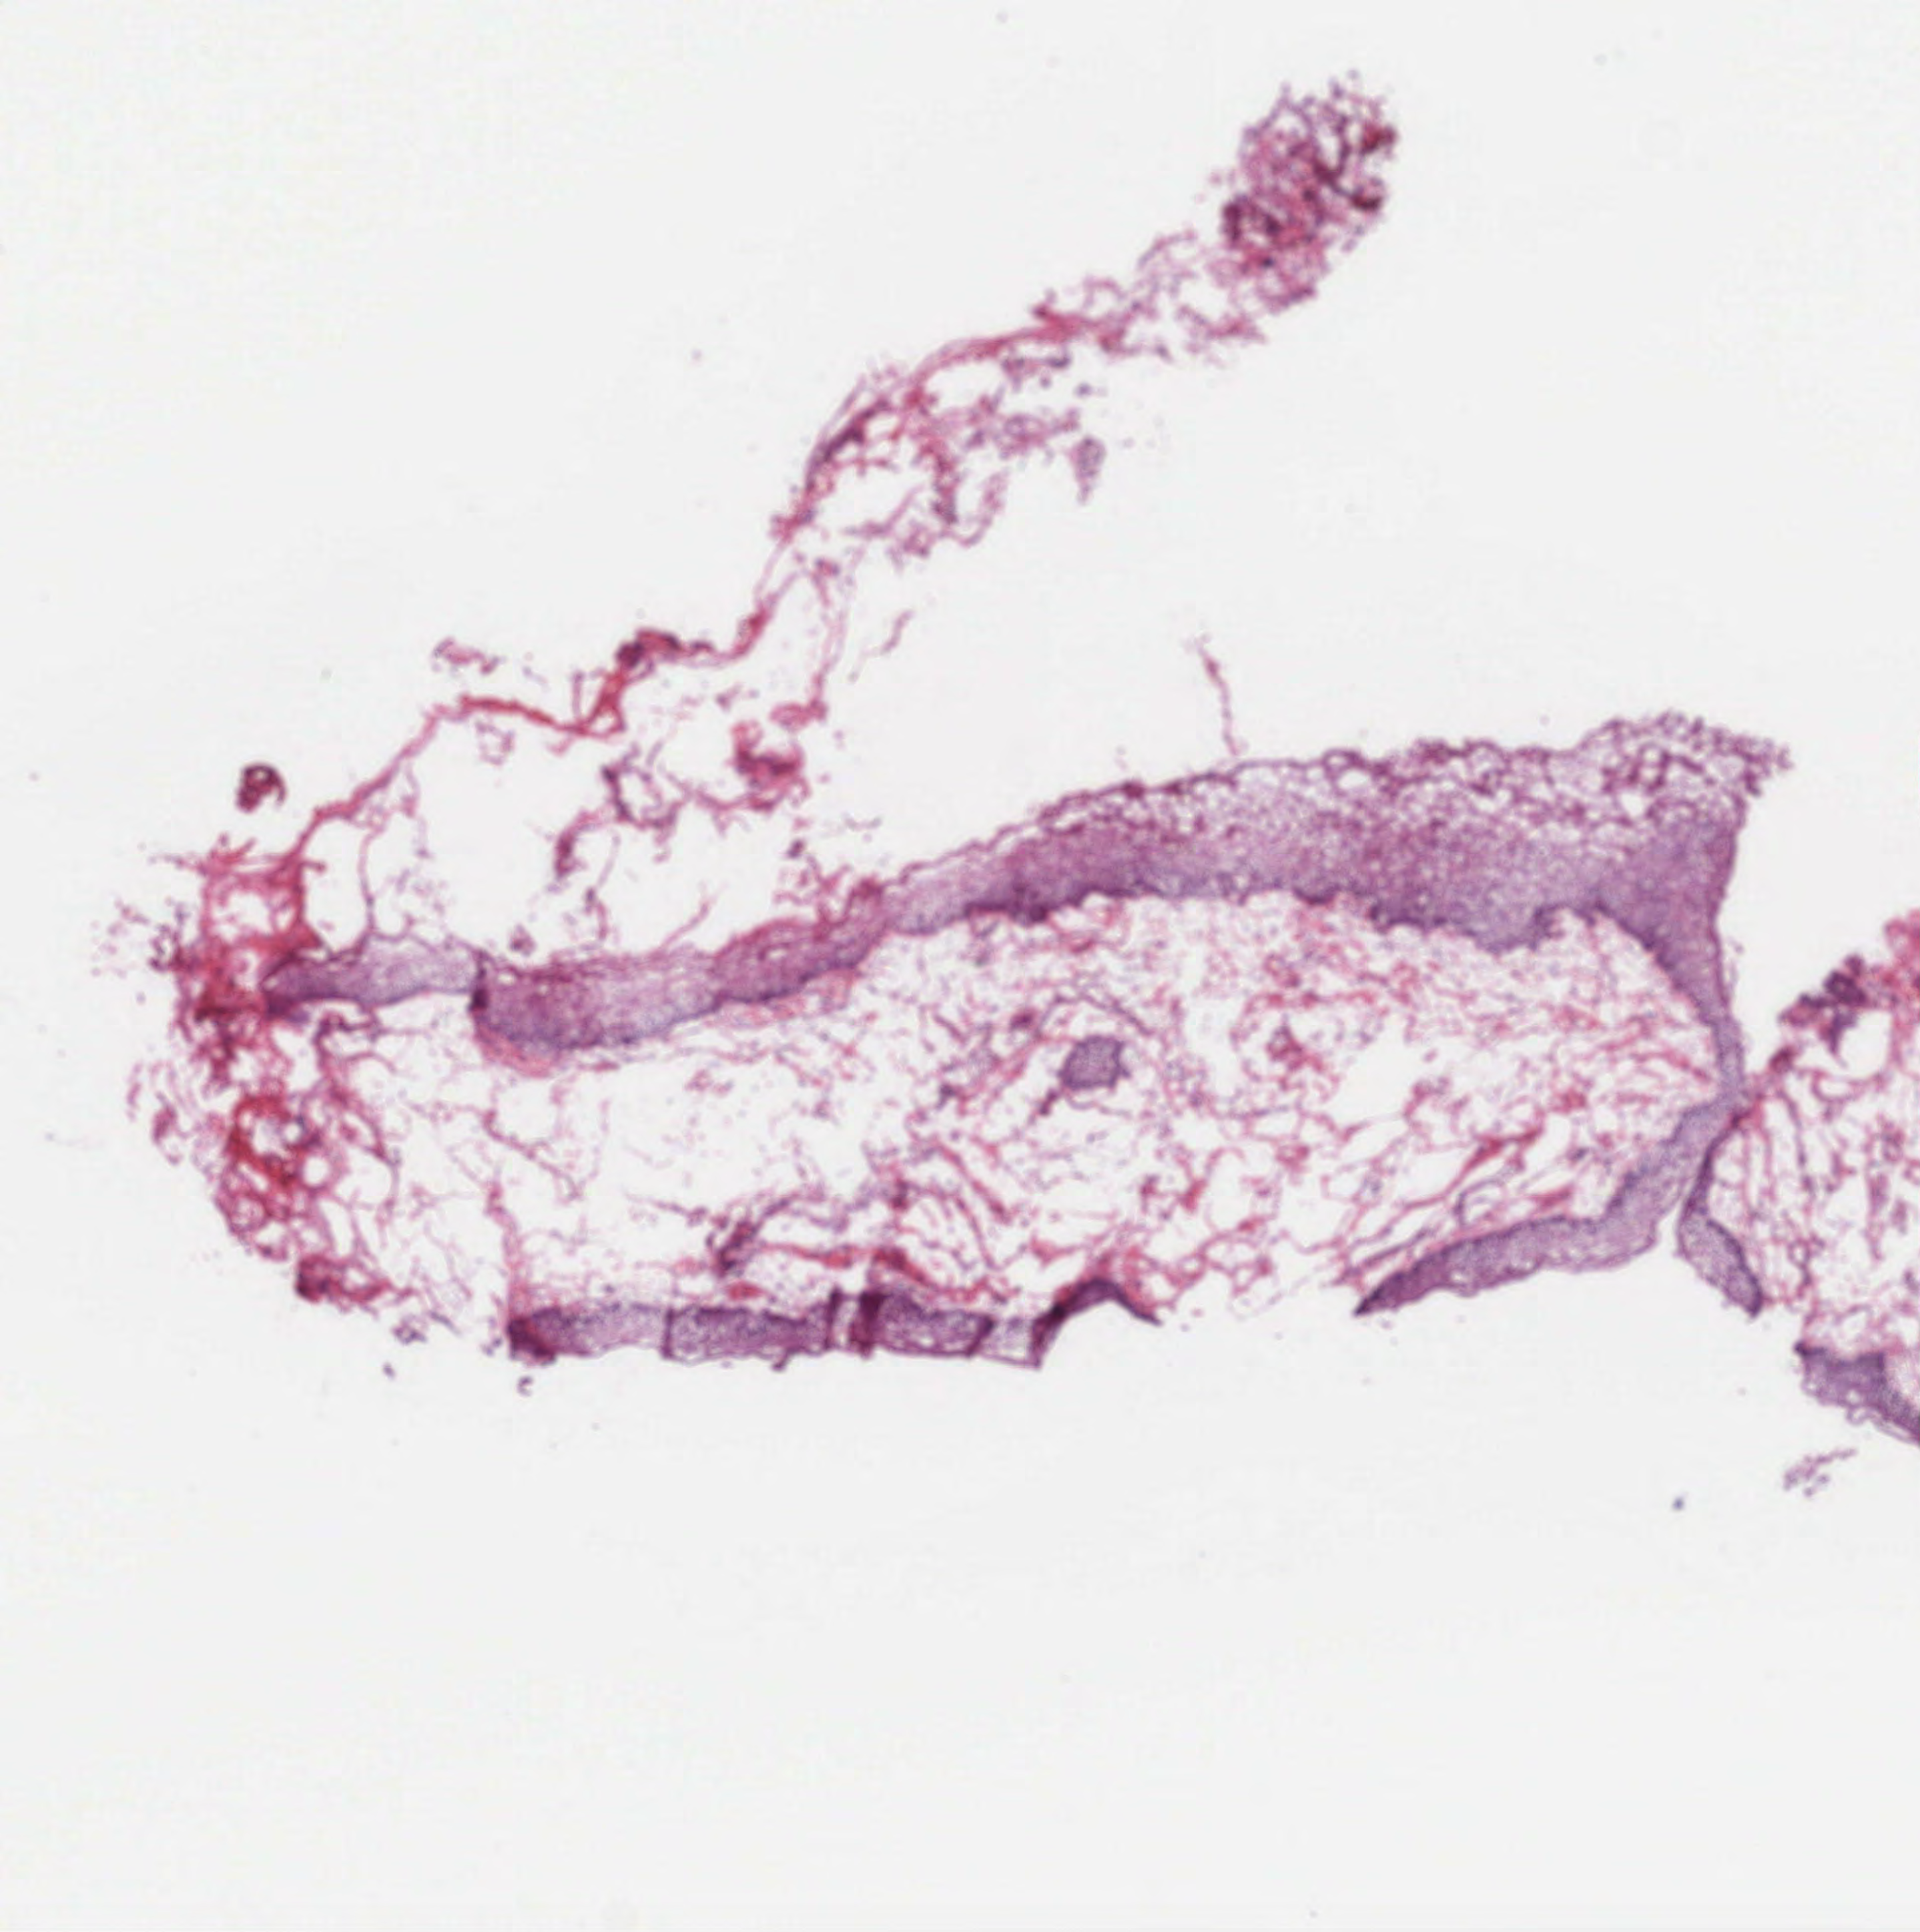
Whole-slide histology image, Hematoxylin and eosin (H&E) stained, a low-resolution overview of the entire scanned area, about 5.8 x 5.8 mm (from a 40x scan); frozen section from the top of the tissue portion; sample: solid tissue normal (non-tumour tissue), head and neck. Female patient; age at initial diagnosis 60 years.
This section: solid tissue normal (non-tumour) sample from the same patient. Patient diagnosis: Squamous cell carcinoma, NOS (larynx, NOS).